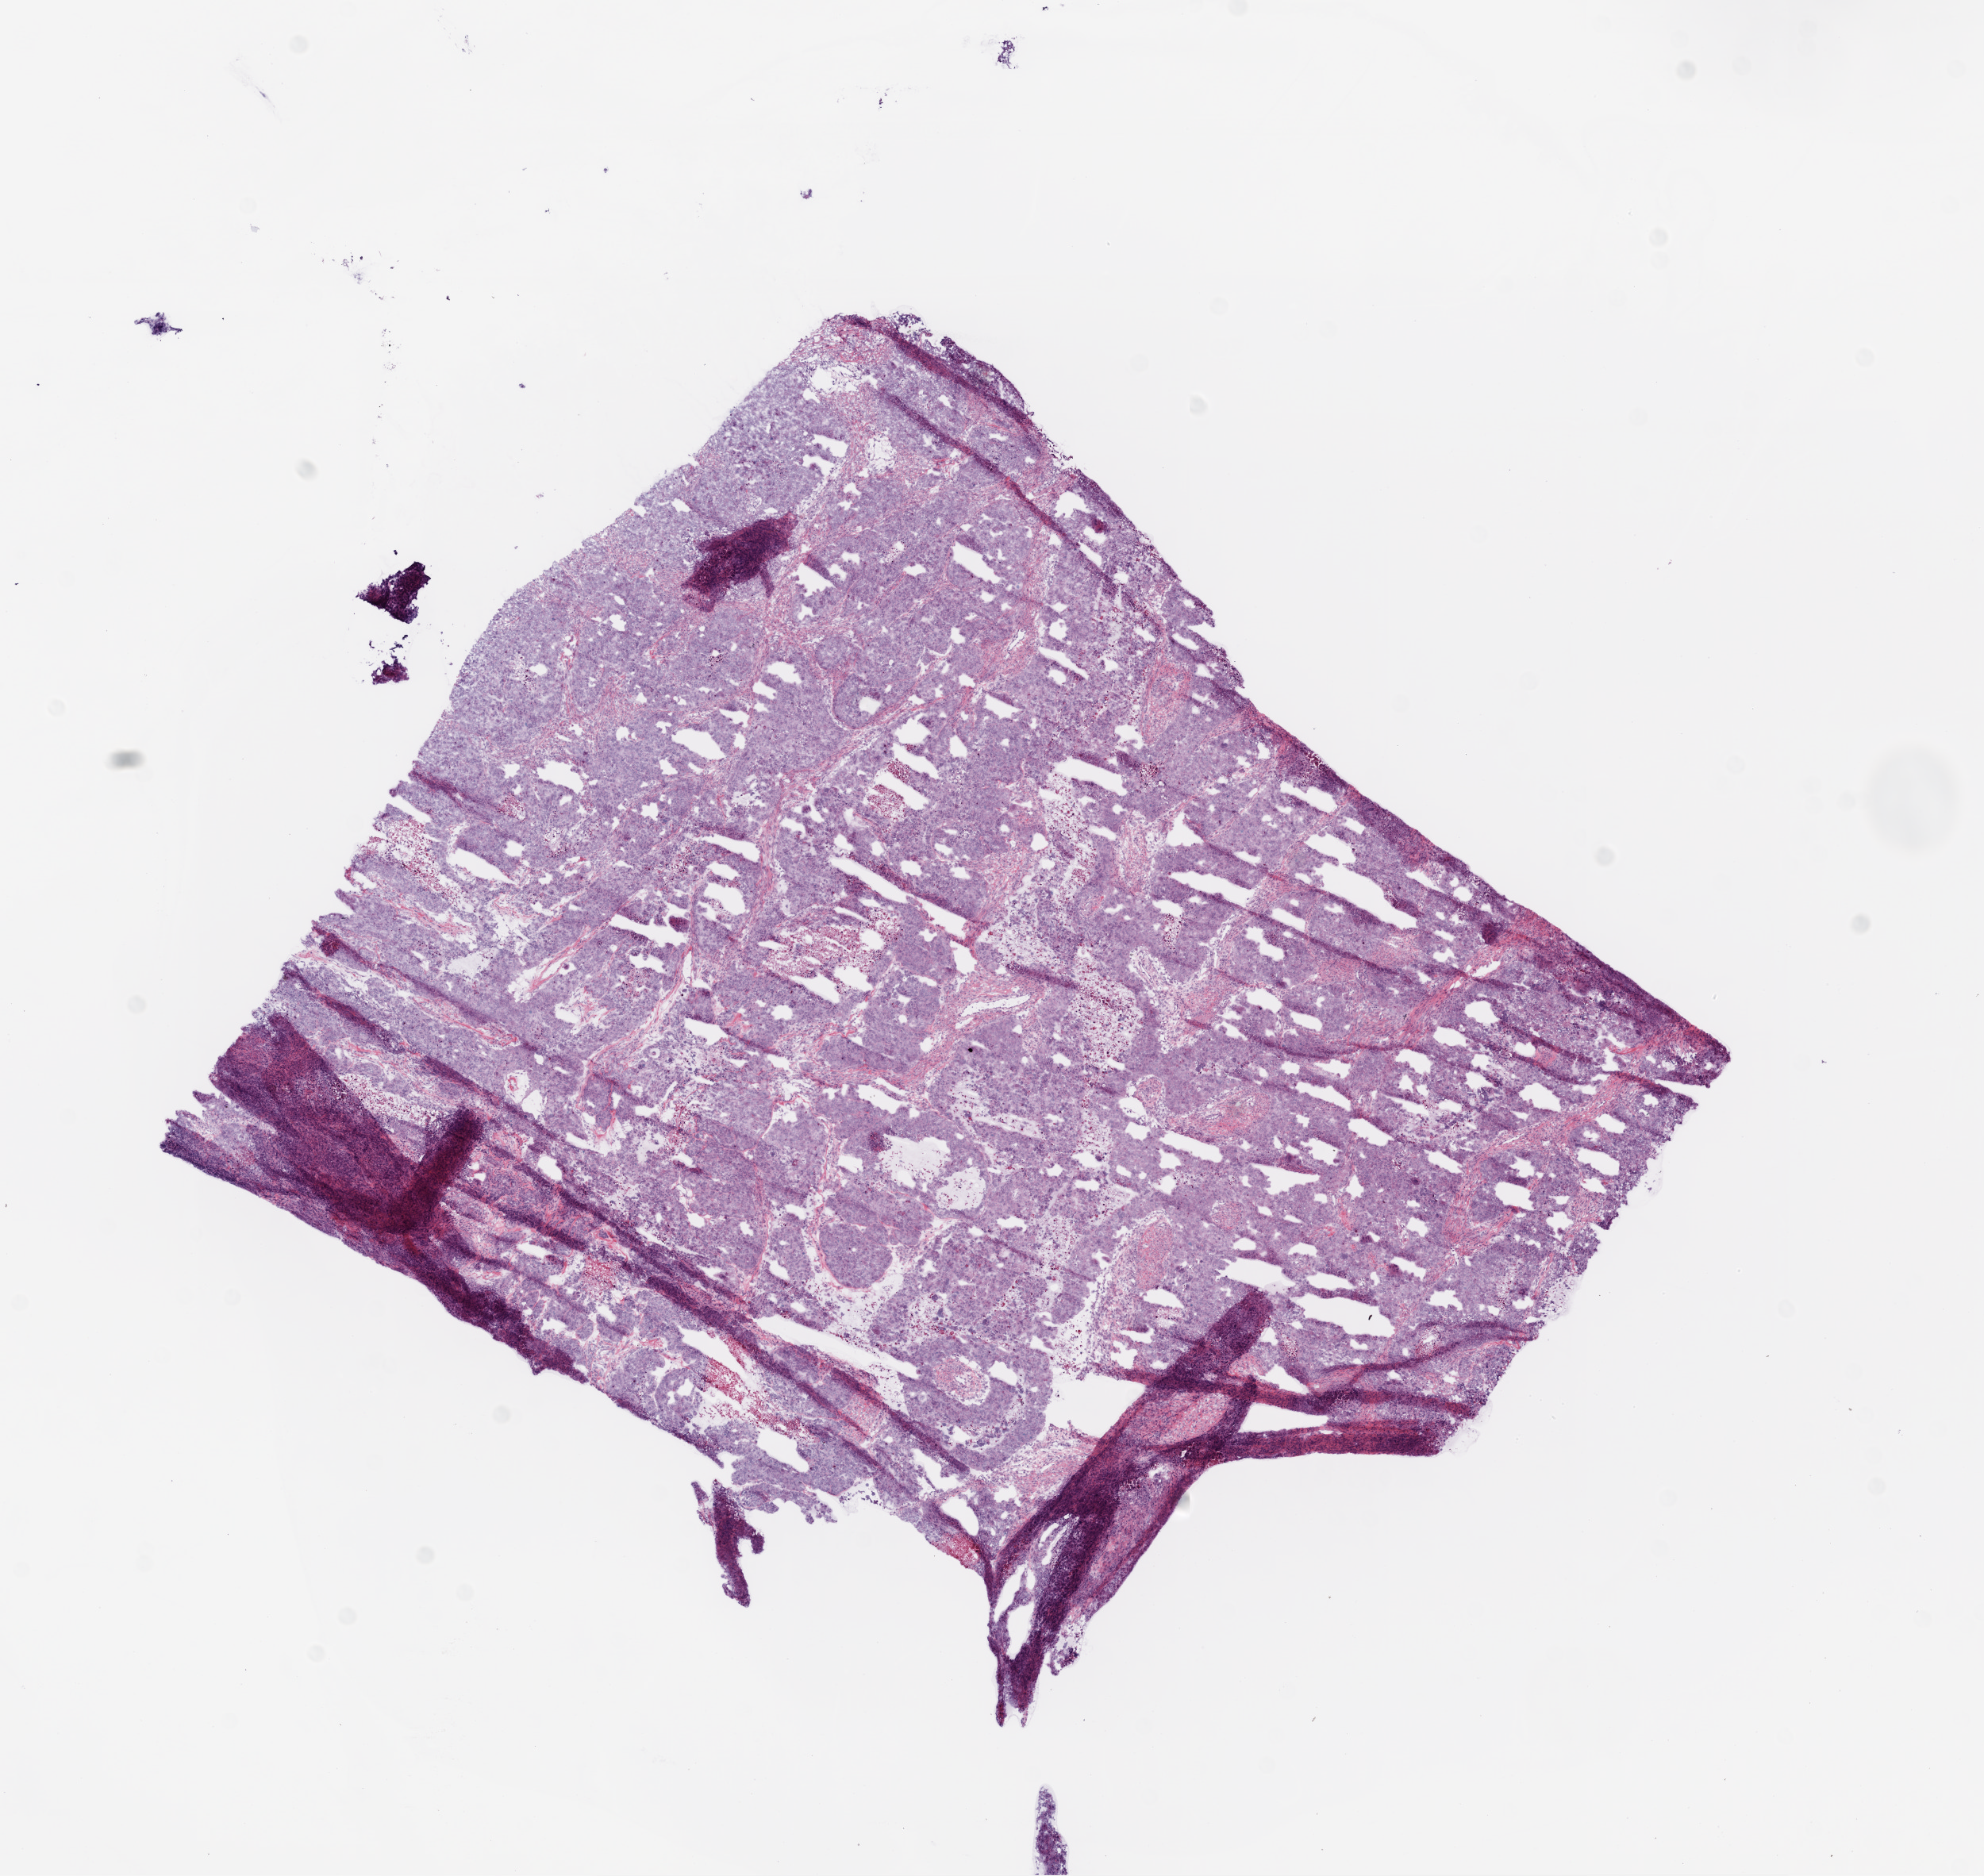
Whole-slide histology image, Hematoxylin and eosin (H&E) stained, low-resolution overview of the scanned area, about 10.0 x 9.5 mm (from a 20x scan). Frozen section from the bottom of the tissue portion. Sample: primary tumour, ovary. Female, age 63 years at initial diagnosis. Histologic grade: G3 (poorly differentiated). Composition of this section per pathologist review: tumour cells 70%, tumour nuclei 80%, normal cells 0%, stromal cells 20%, necrosis 10%.
Histologic diagnosis: Serous cystadenocarcinoma, NOS. FIGO stage: IIC.